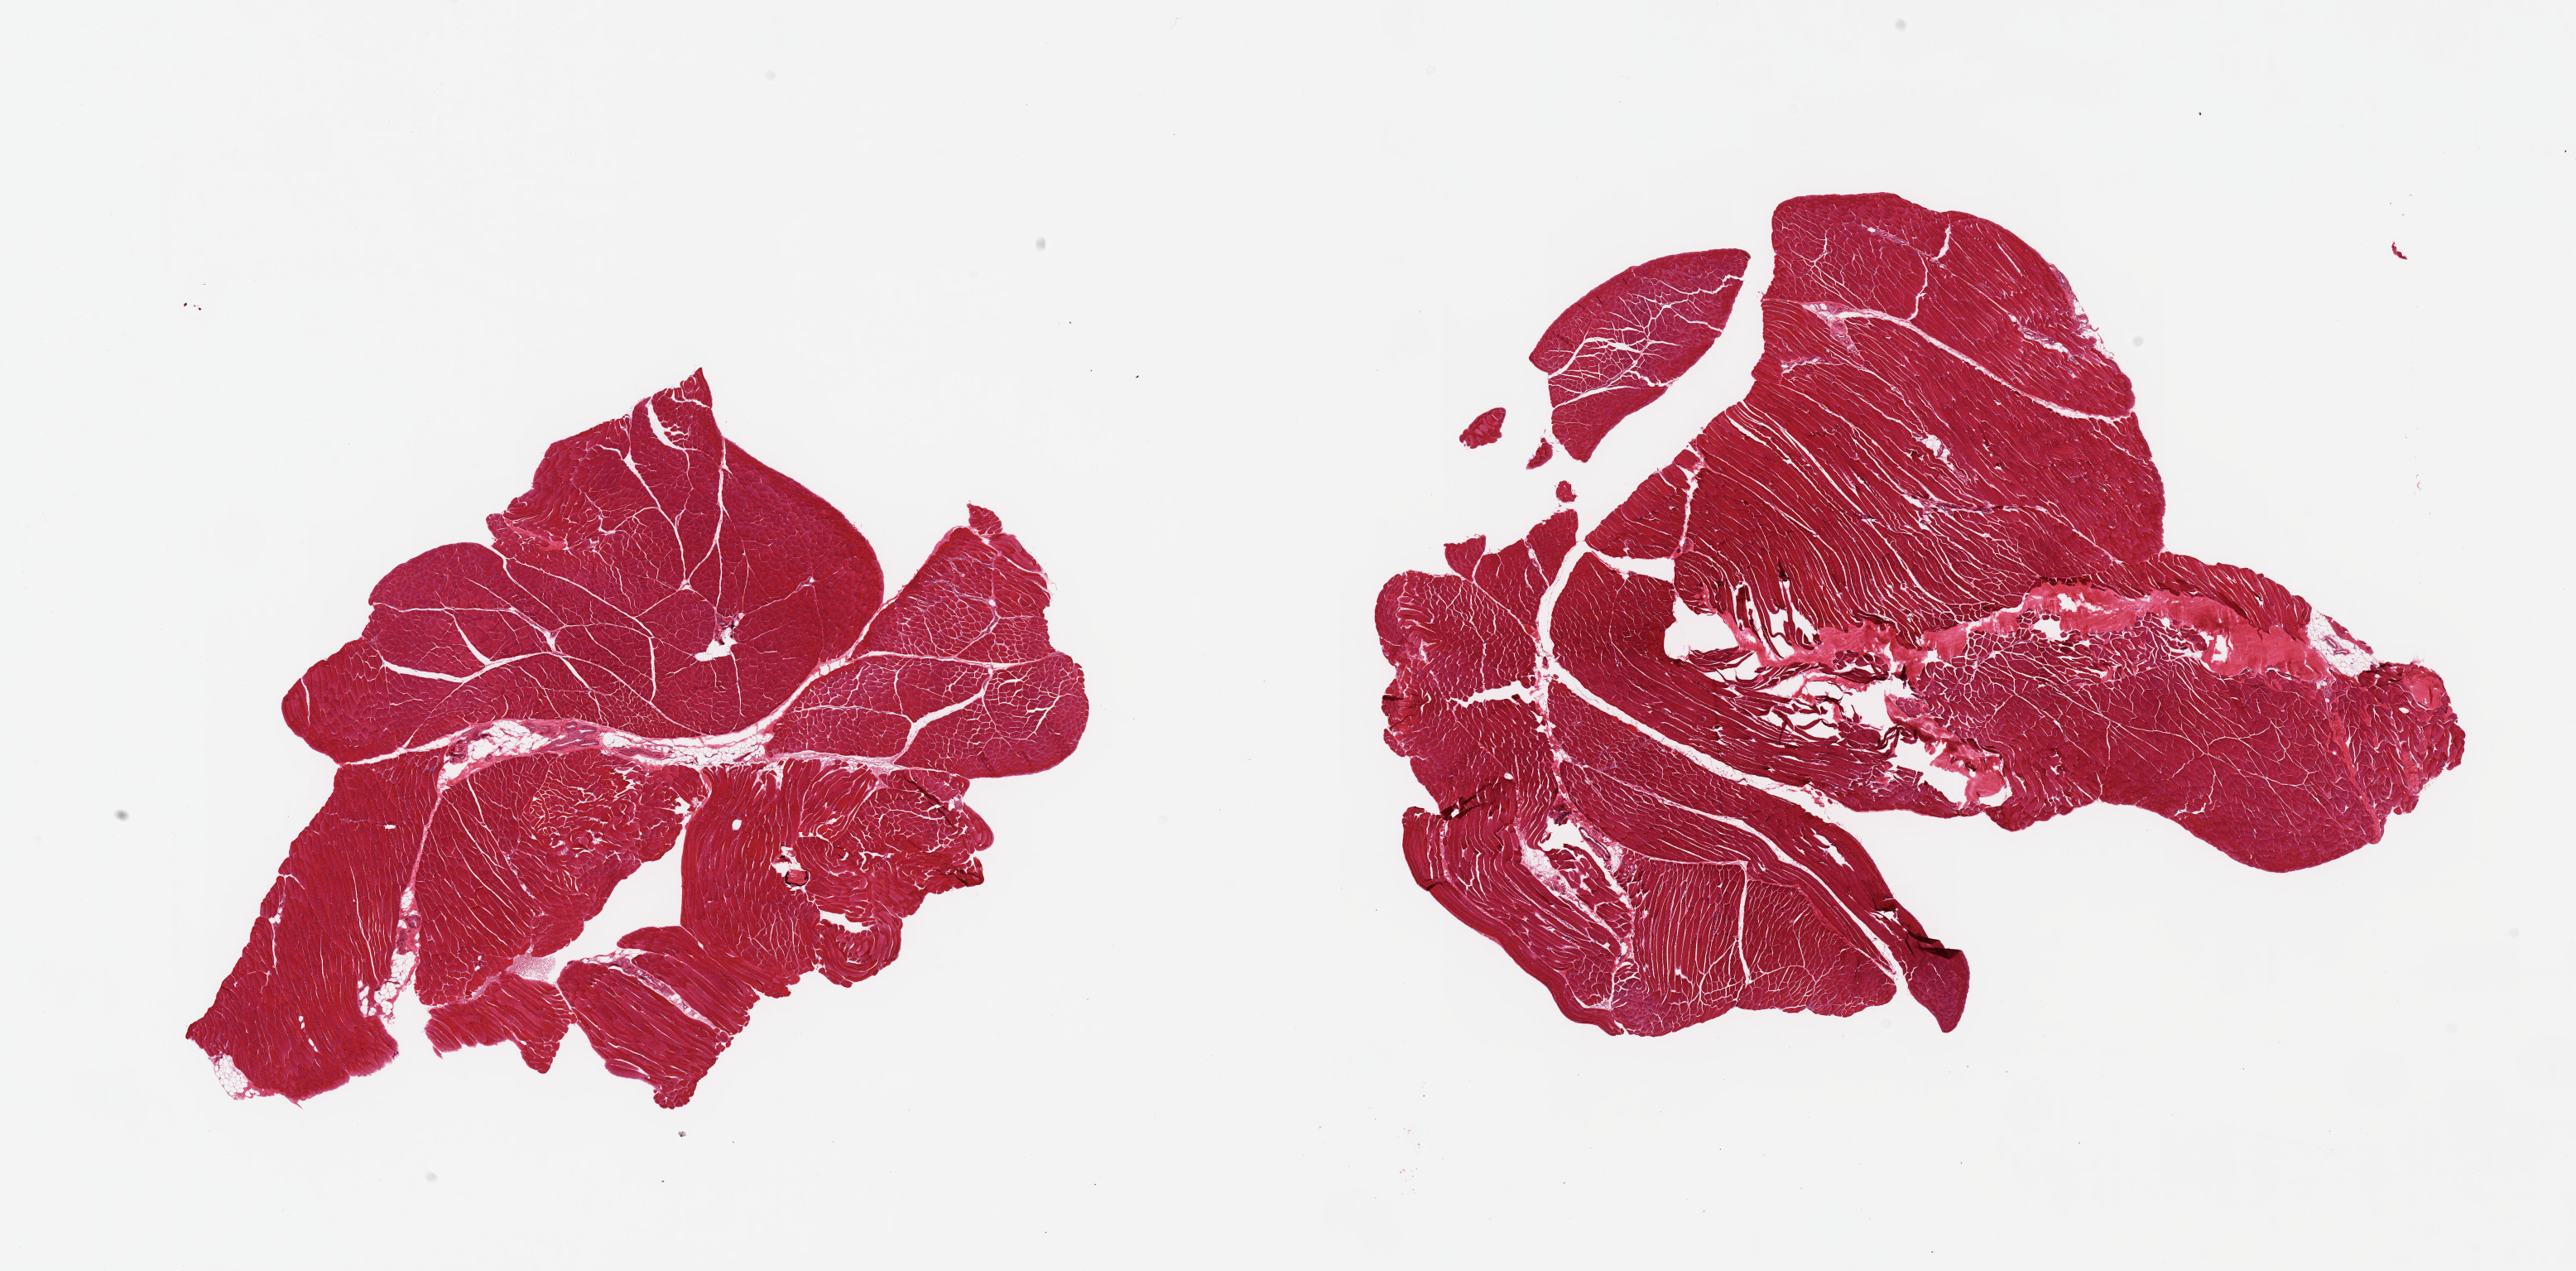
Digitized hematoxylin and eosin (H&E)-stained section, a low-resolution overview of the entire scanned area, about 24.6 x 12.1 mm. PAXgene-fixed, paraffin-embedded tissue. Target tissue: skeletal muscle. Donor tissue sample. Donor sex: male.
Pathologist's review note for this sample: 2 pieces, ~10% tendon insertion/fascia/adipose elements.